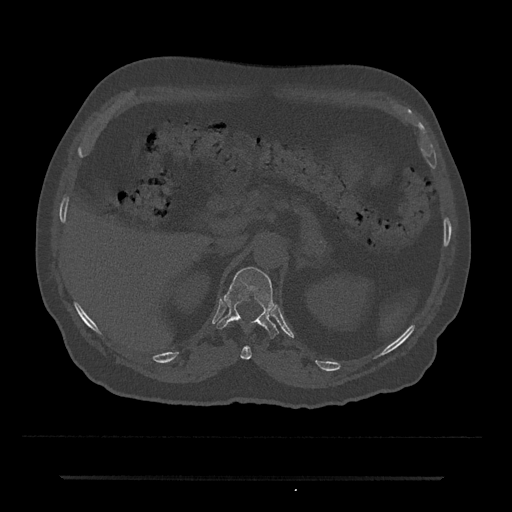
CT including the spine, one axial slice; slice 140 of 797 in the series (ordered by position); reconstruction kernel Br40s/3; 120 kVp; bone window (W 1800 / L 400 HU); 0.5 mm slice thickness; 512 × 512 image matrix, field of view 437 × 437 mm. Patient: male, 69 years. From the clinical record (not read from this slice): primary cancer: prostate.
Annotated regions visible in this slice (semi-automatic segmentation, software-assisted and operator-edited):
- T11 vertebra: bounding box [x1, y1, x2, y2] px = [231, 320, 252, 360]
- T12 vertebra: [216, 267, 279, 338]